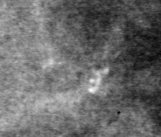
Cropped region of a digitized screen-film mammogram centred on a radiologist-marked abnormality; left breast; MLO view.
Finding: calcifications, morphology pleomorphic, distribution clustered; BI-RADS assessment category 4; subtlety rating 2 on a 1 (subtle) to 5 (obvious) scale; pathology result (as recorded, not read from the image): benign.